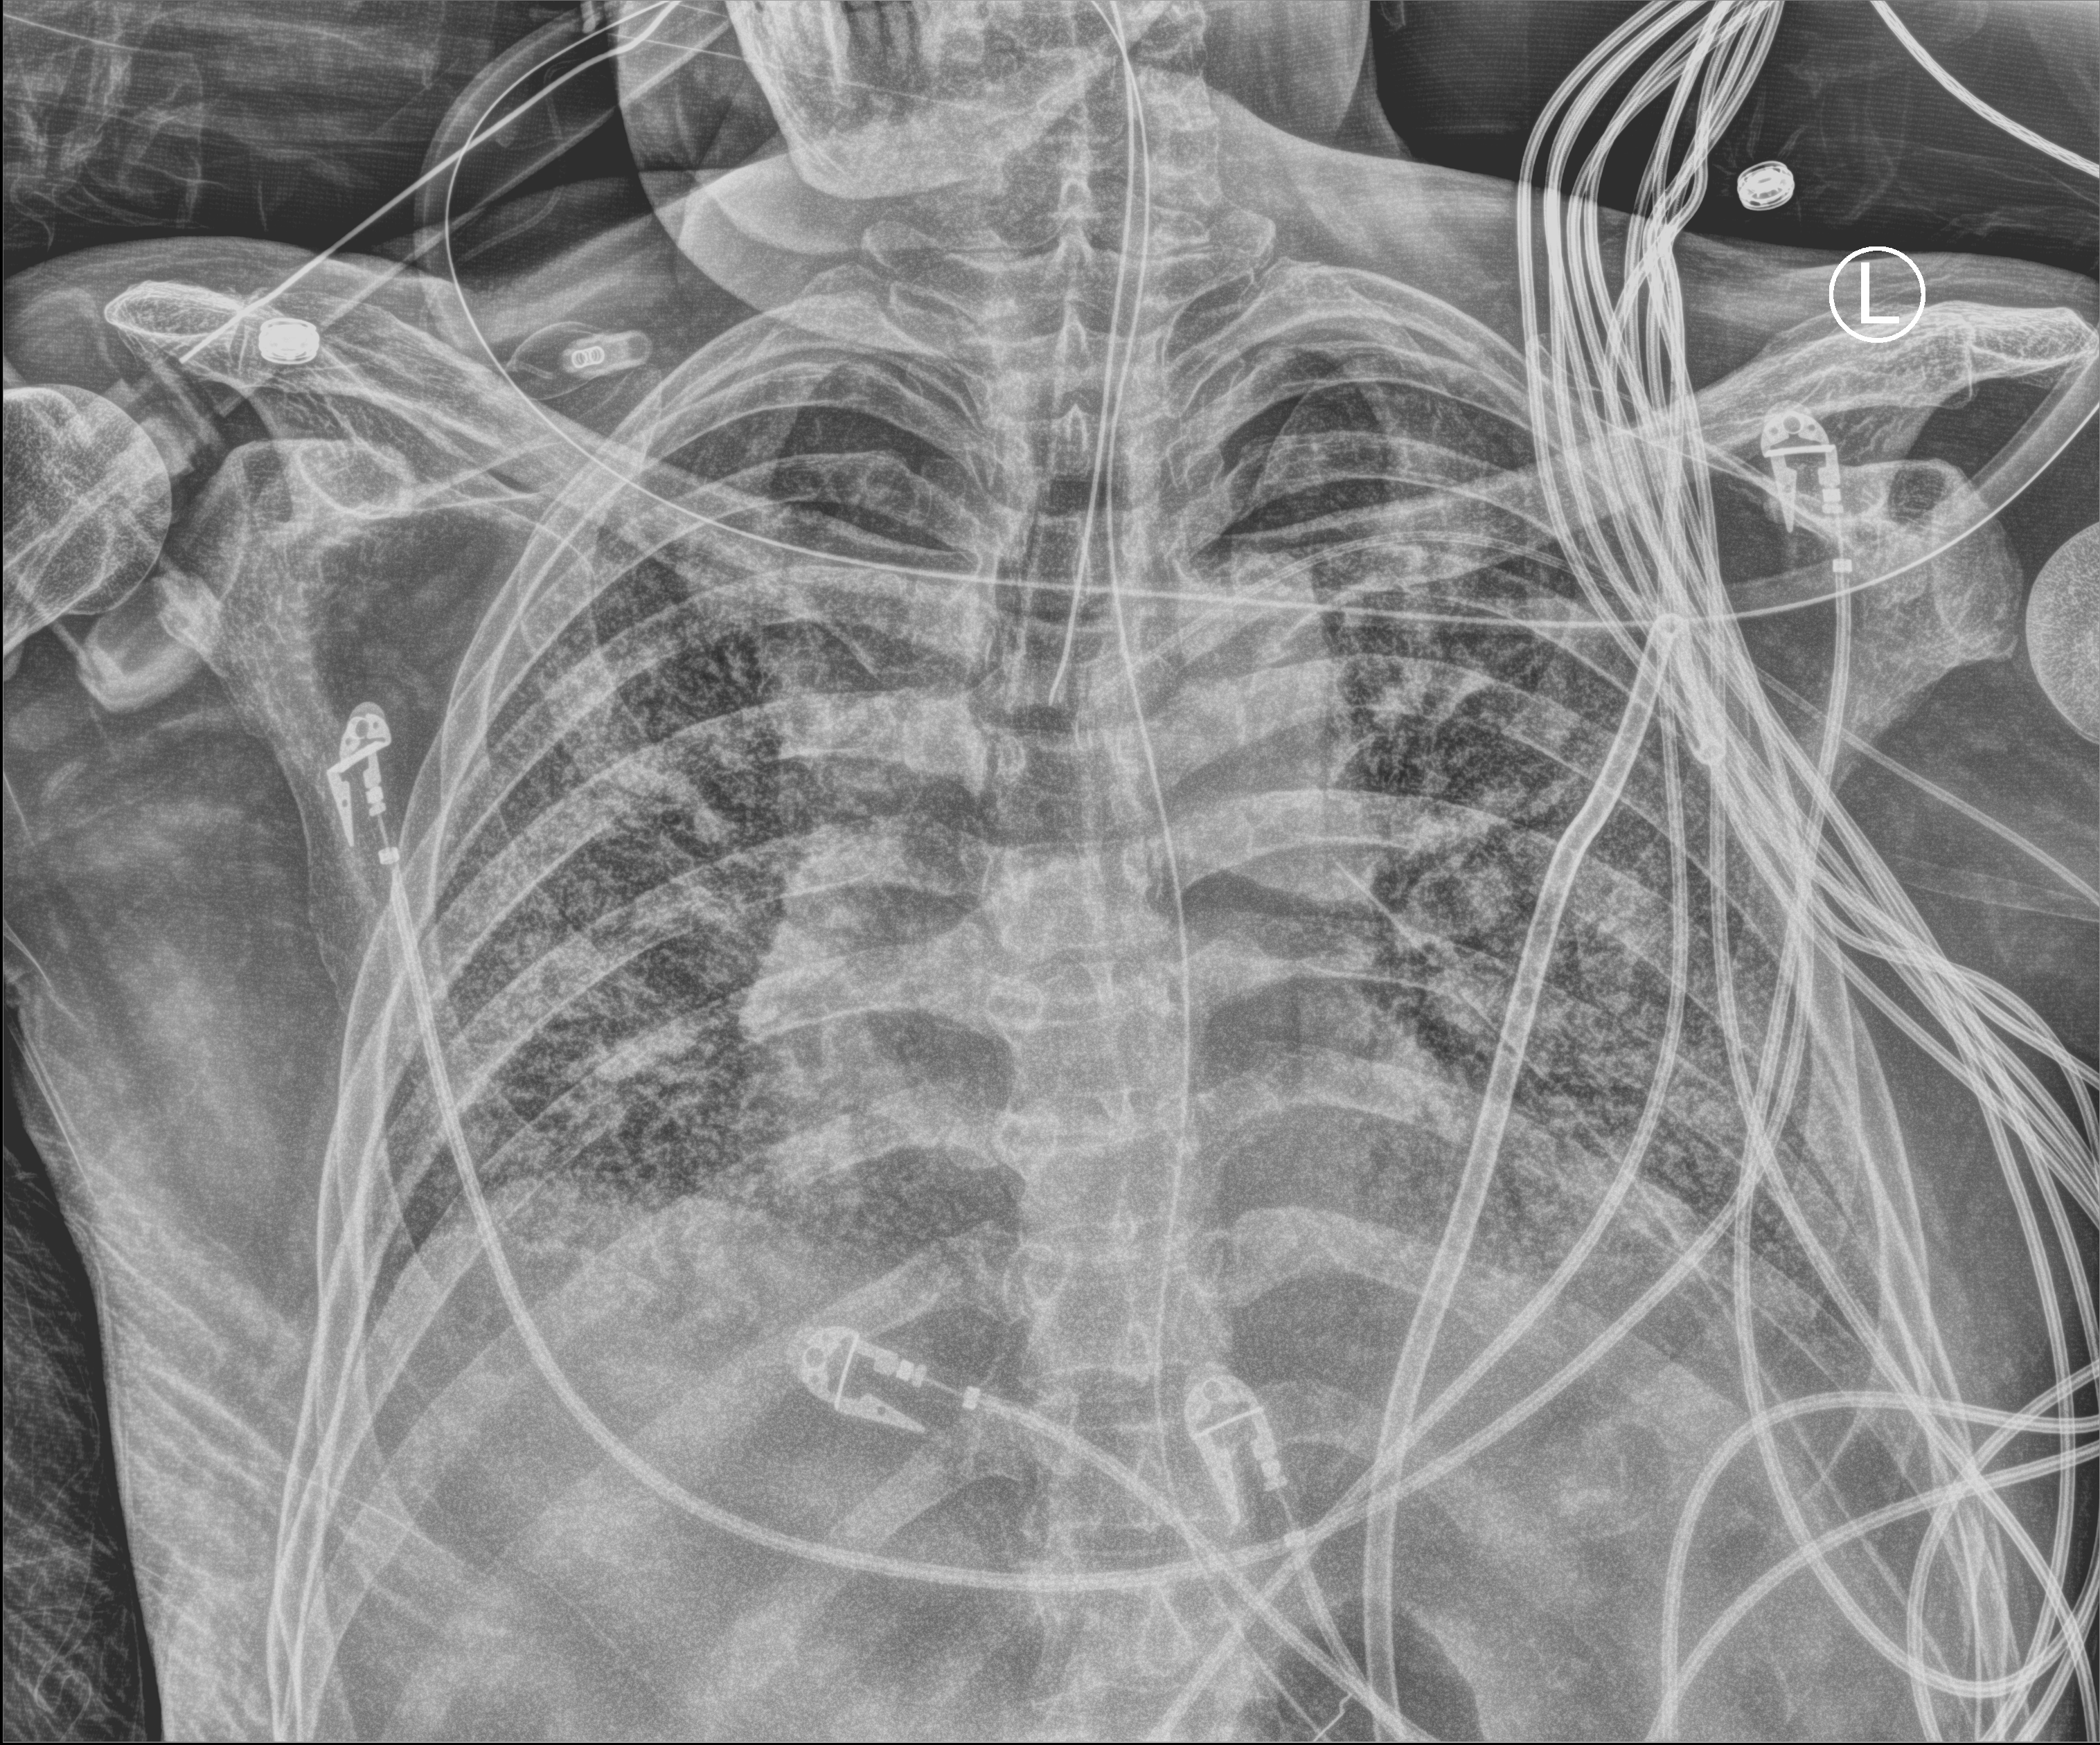
Chest X-ray (portable); anteroposterior (AP) projection. Male patient hospitalised with COVID-19, age 60–74 years.
From the hospital-stay record, not from the radiograph (when in the stay this image was taken is not recorded): mechanically ventilated during this hospital stay: yes; length of hospital stay: 54 days; admitted to intensive care during this hospital stay: yes.